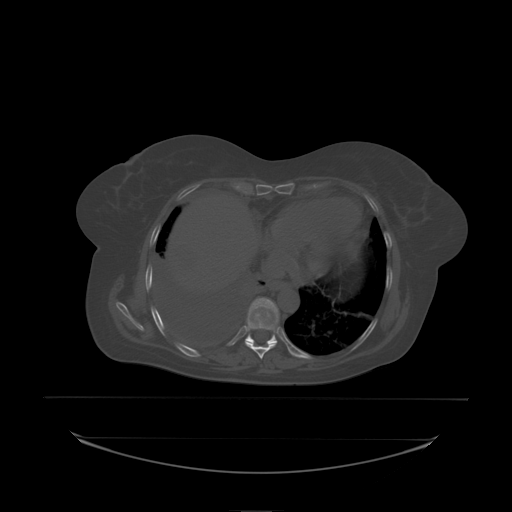
CT including the spine, one axial slice; position 129 of 242 along the scan axis; bone window (W 1800 / L 400 HU); 2.5 mm slice thickness; 512 × 512 image matrix, field of view 500 × 500 mm. Patient: female, 53 years. From the clinical record (not read from this slice): primary cancer: lung.
Outlined on this slice (semi-automatically segmented with operator editing):
- T8 vertebra: bounding box (x1, y1, x2, y2) in pixels: (247, 309, 279, 332)
- T9 vertebra: (248, 298, 279, 338)